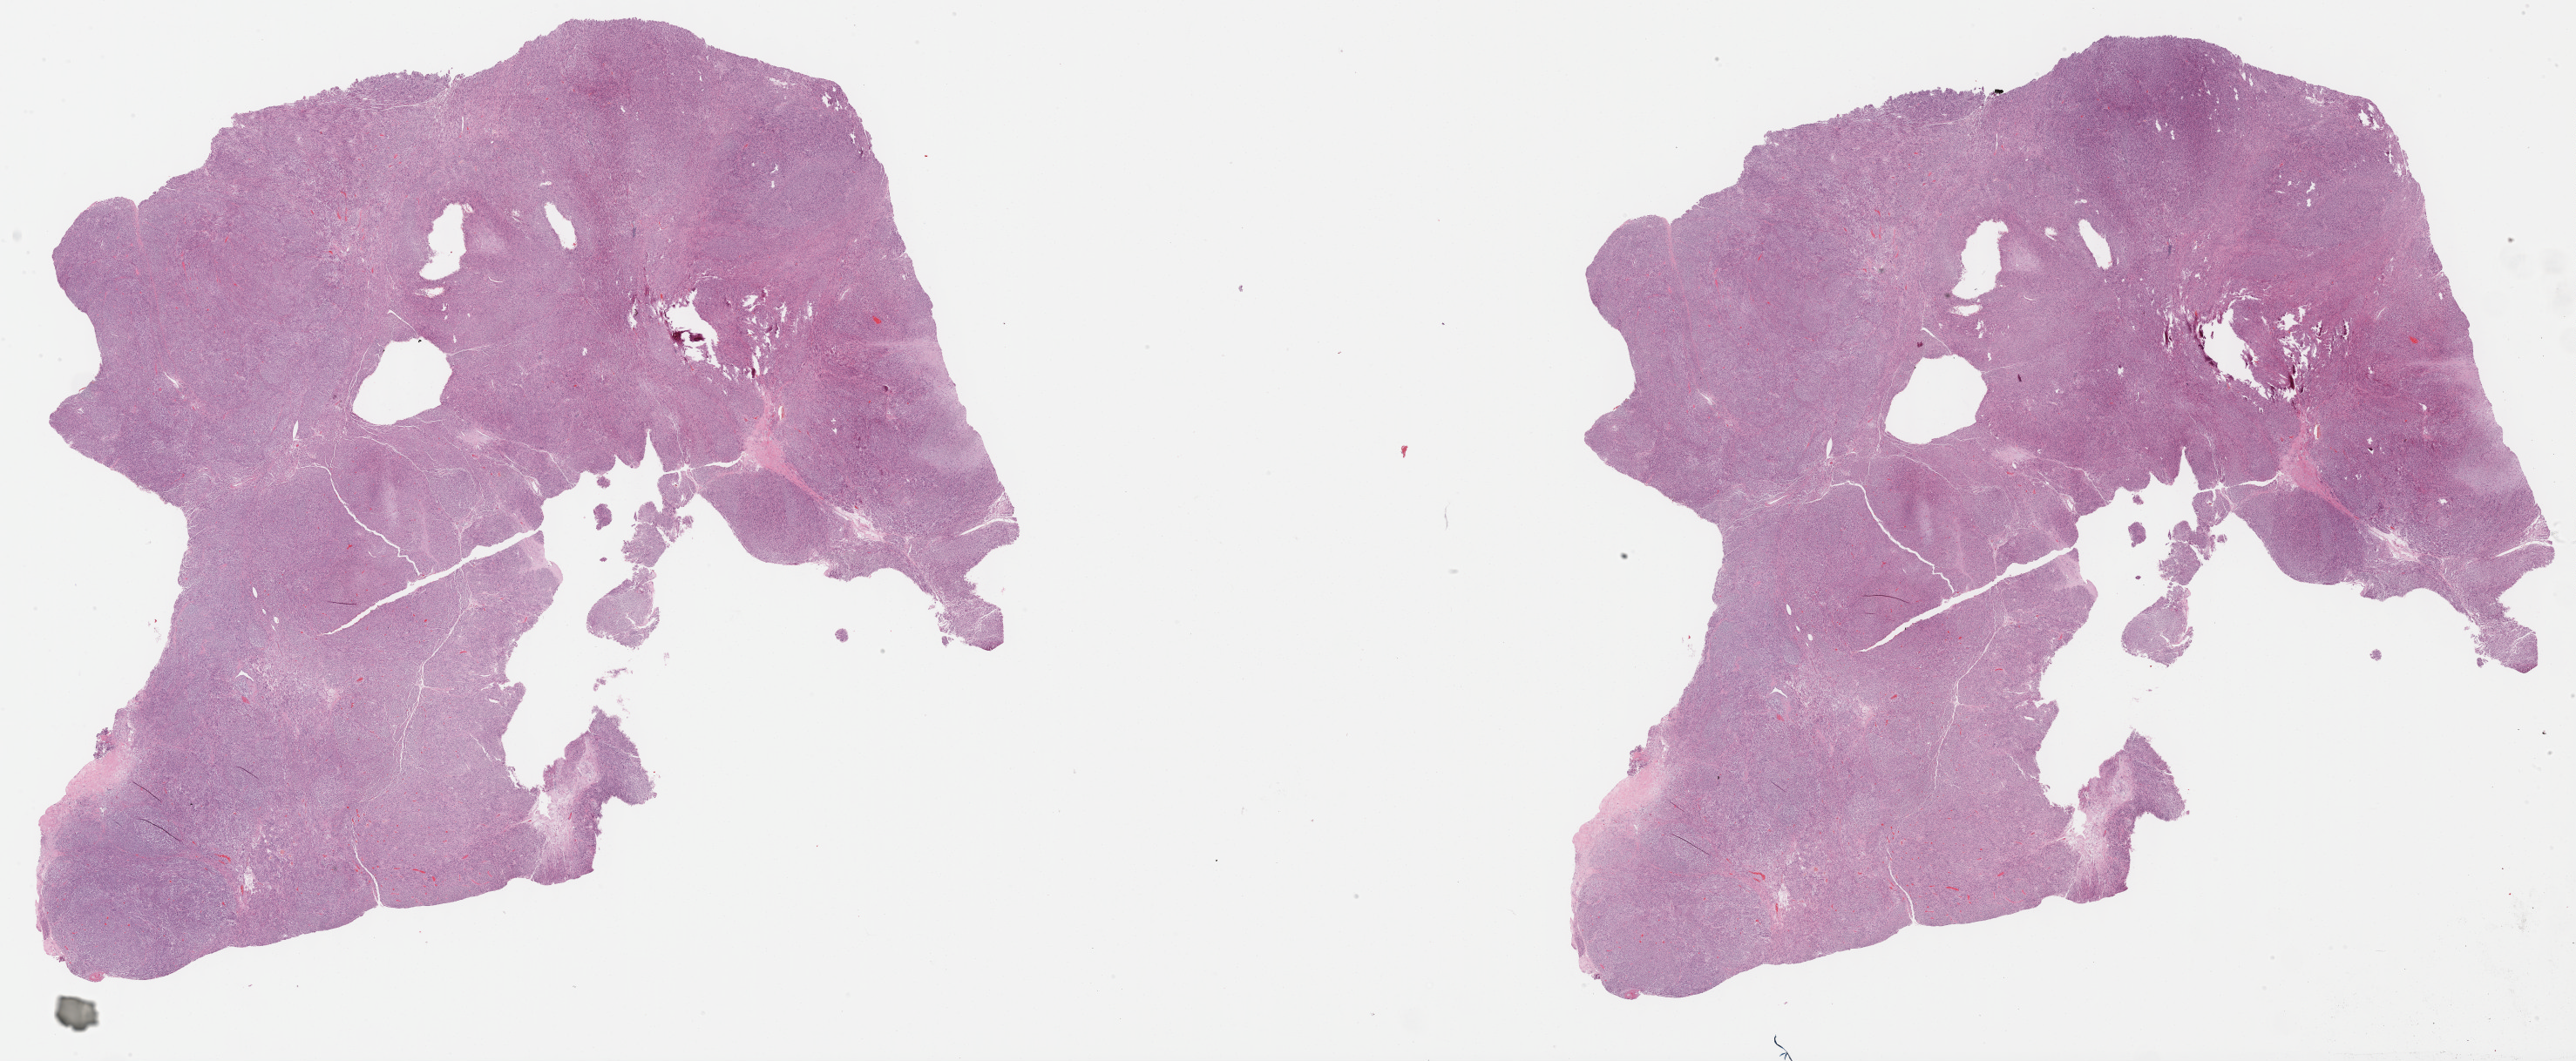
H&E-stained whole-slide image — shown as a low-resolution overview of the whole scanned area (about 47.8 x 19.7 mm). Formalin-fixed paraffin-embedded (FFPE) diagnostic section. Primary tumour sample from the retroperitoneum and peritoneum. Patient: male, age at initial diagnosis 78 years.
Diagnosis: Leiomyosarcoma, NOS (retroperitoneum).